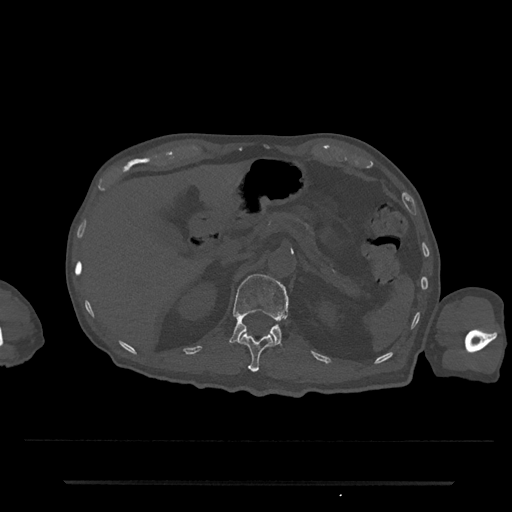
CT including the spine, one axial slice; slice 162 of 797 in the series (ordered by position); reconstruction kernel Br40s/3; 120 kVp; bone window (W 1800 / L 400 HU); 0.5 mm slice thickness; 512 × 512 image matrix, field of view 427 × 427 mm. Male patient, age 74 years. Case-level facts recorded for this patient, not image findings: primary cancer: prostate.
Annotated regions visible in this slice (semi-automatically segmented with operator editing):
- L1 vertebra: box from (x=230, y=274) to (x=289, y=346) px
- T12 vertebra: (x=240, y=333)–(x=273, y=372)